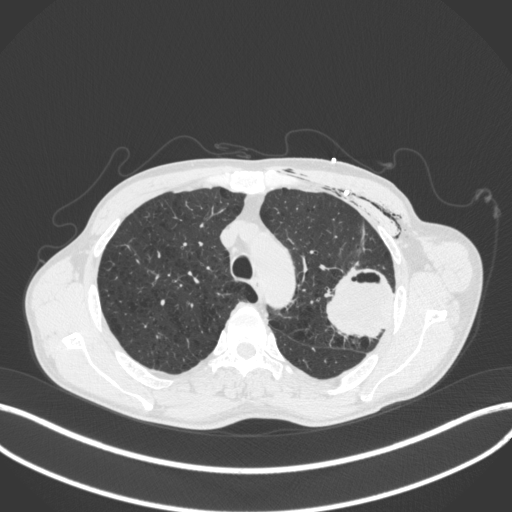
Chest CT, one axial slice; slice 304 of 416 in the series (ordered by position); reconstruction kernel B31f; lung window (W 1500 / L -600 HU); 1 mm slice thickness; 512 × 512 image matrix, field of view 400 × 400 mm. Male patient, age 58 years. Case-level facts recorded for this patient, not image findings: clinical TNM (as recorded): T3 N0 M0.
Structures marked on this image (bounding box drawn by a radiologist):
- lung tumour (recorded histology: adenocarcinoma): bounding box <323,266,399,351> (left, top, right, bottom; pixels)